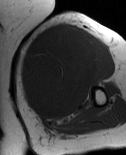
MRI of an extremity soft-tissue mass, one axial slice. Slice 44 of 86 in the series (ordered by position). MR volume resampled by the dataset authors to the PET/CT grid (not the native acquisition matrix). 3.27 mm slice thickness. 126 × 155 image matrix, field of view 123 × 151 mm. Female patient. From the clinical record (not read from this slice): histological type: pleiomorphic leiomyosarcoma; grade: high; site of the primary tumour: left biceps.
Outlined on this slice (expert contour drawn on MRI and transferred to this co-registered scan by the dataset authors):
- gross tumour volume including surrounding oedema: box from (x=20, y=26) to (x=107, y=121) px
- gross tumour volume (mass): (x=20, y=26)–(x=101, y=119)